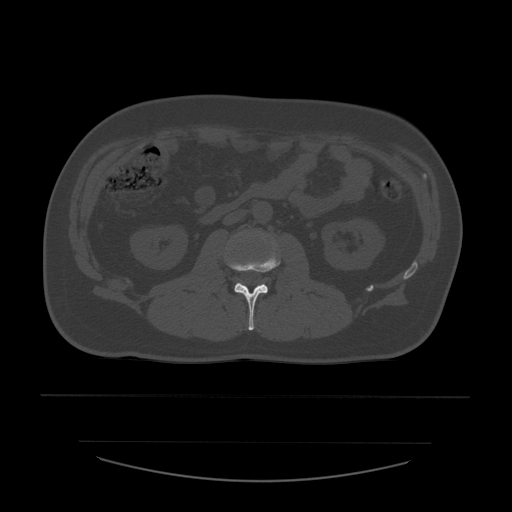
CT including the spine, one axial slice. Slice 192 of 532 in the series (ordered by position). Bone window (W 1800 / L 400 HU). 1.25 mm slice thickness. 512 × 512 image matrix, field of view 441 × 441 mm. Patient age 44 years. From the clinical record (not read from this slice): primary cancer: soft tissue sarcoma.
Structures marked on this image (semi-automatic segmentation, software-assisted and operator-edited):
- L2 vertebra: bounding box <228,235,281,331> (left, top, right, bottom; pixels)